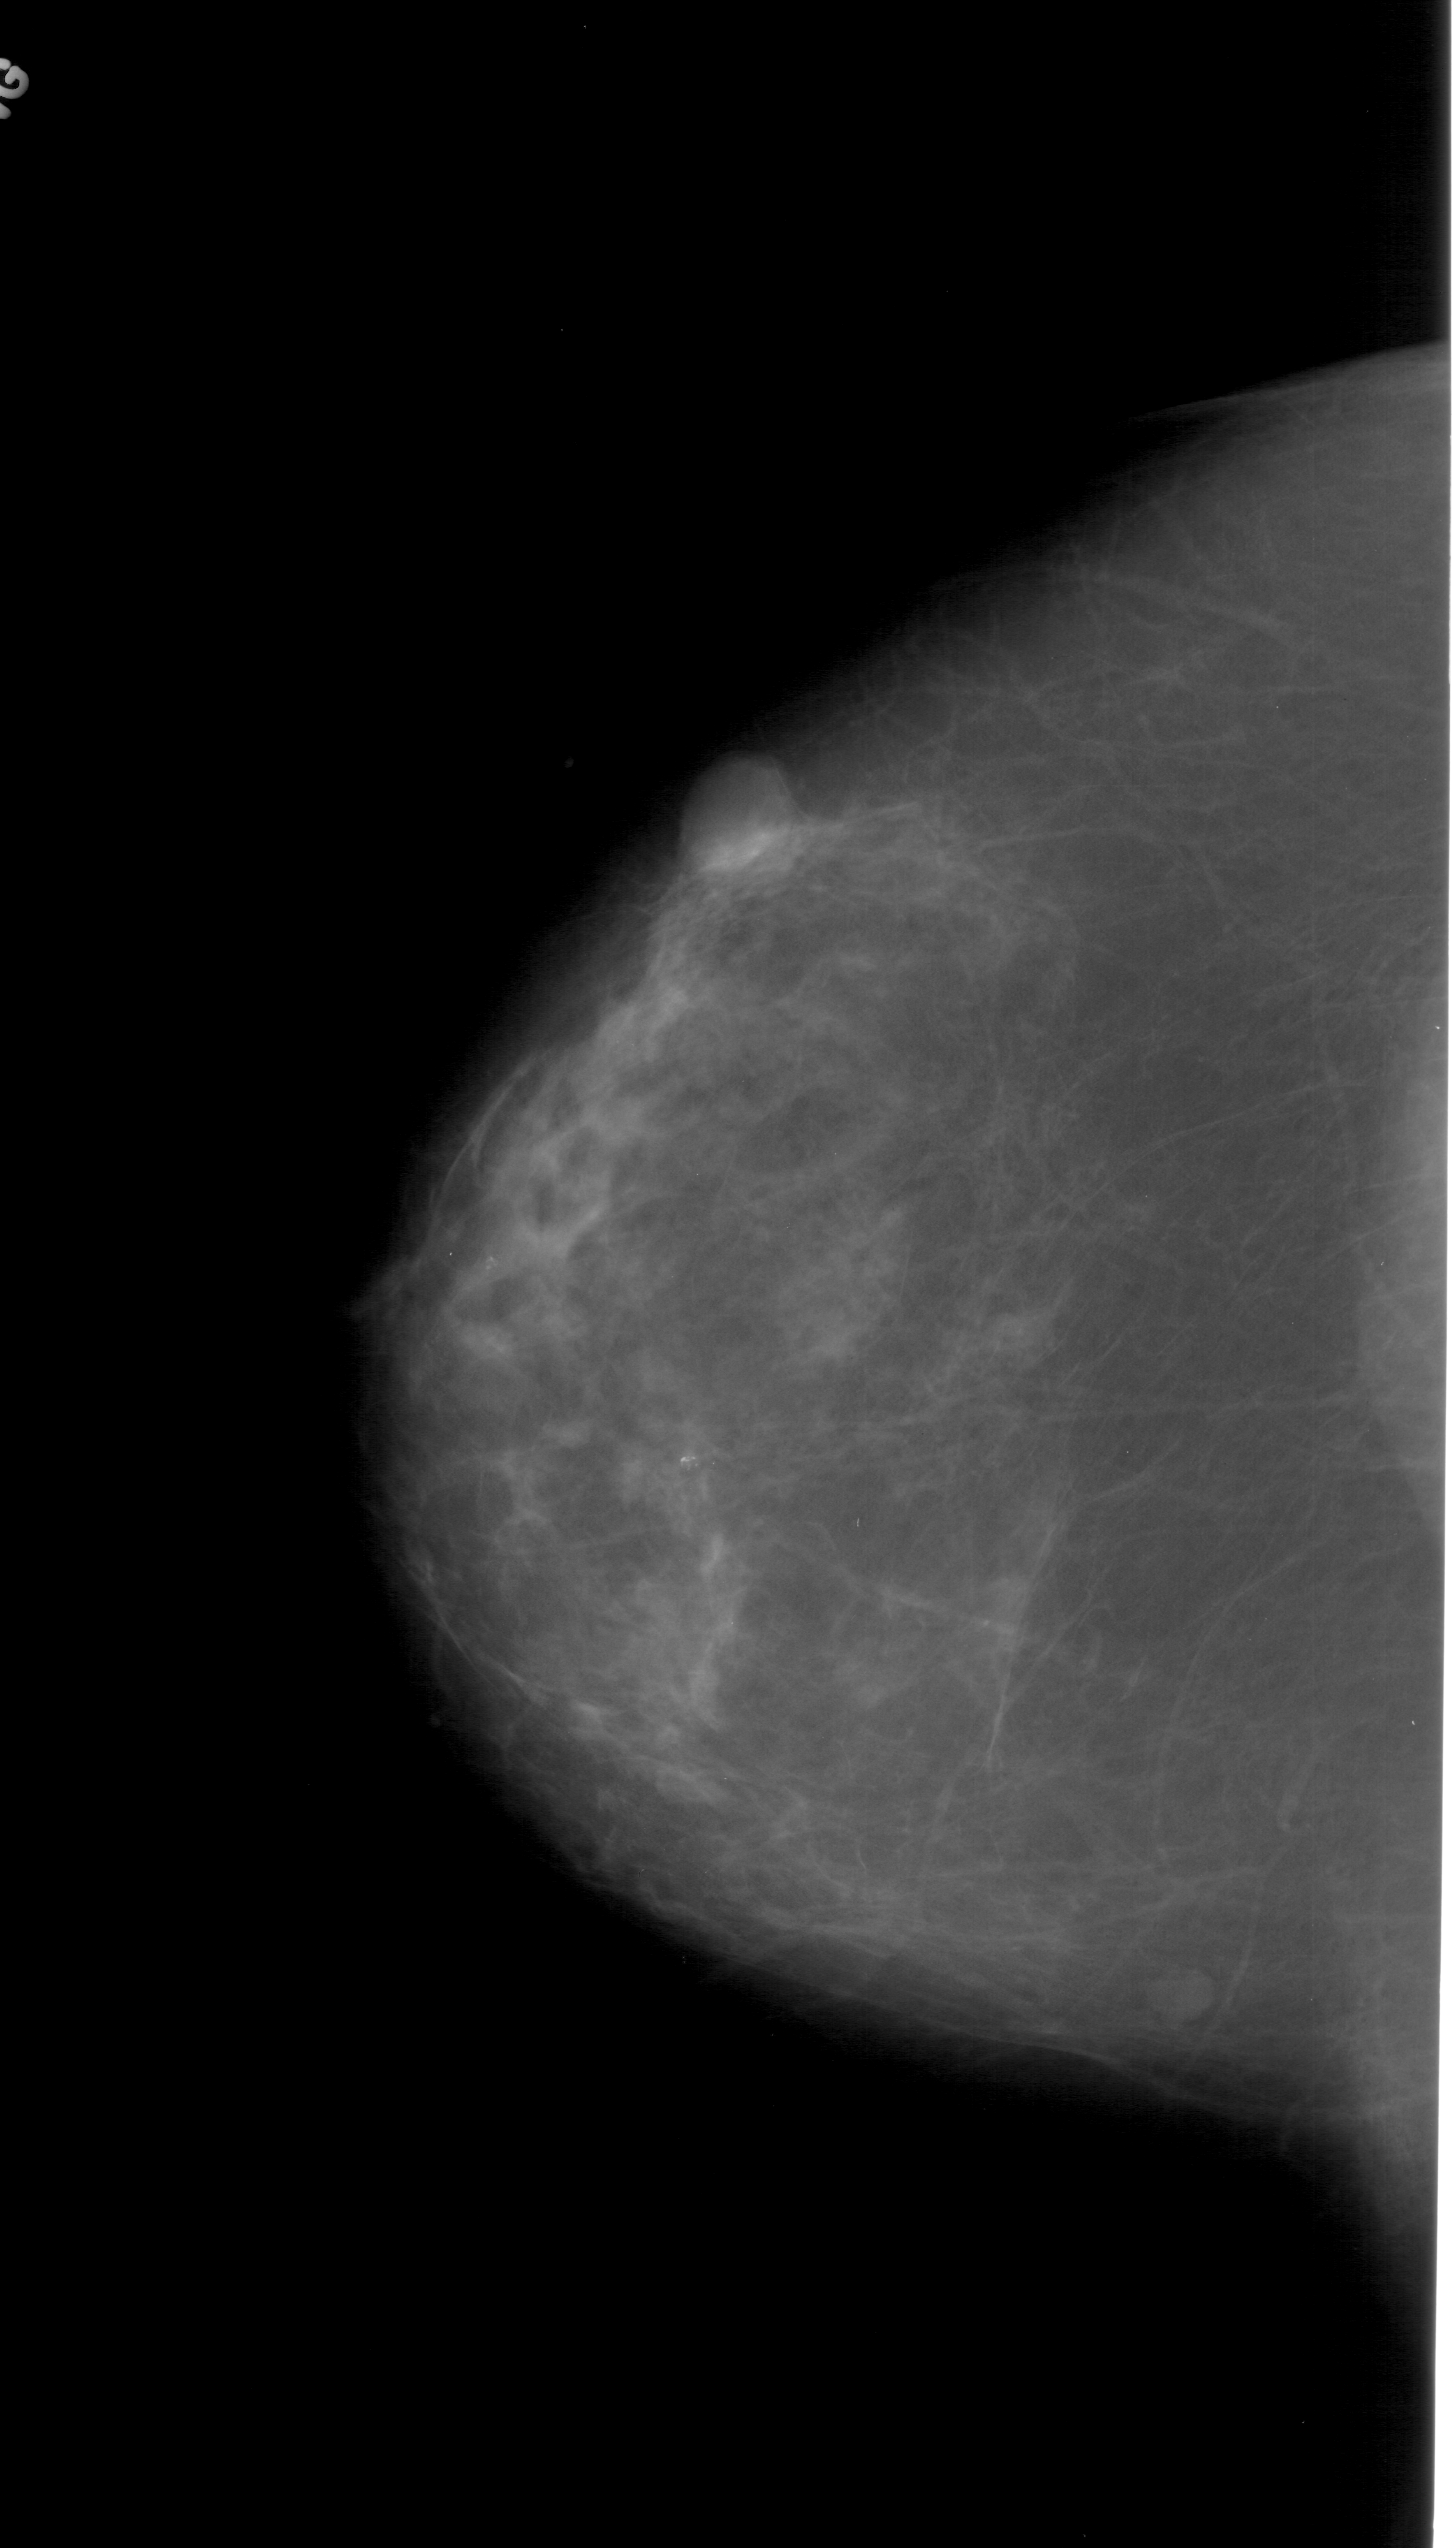
Mammogram (digitized film). Left breast. Craniocaudal (CC) view. BI-RADS breast density category 2 (scale 1–4). 1456 × 2548 image matrix.
Expert-marked regions of interest on this film, with their recorded descriptors:
- mass, shape lobulated, margins circumscribed; BI-RADS assessment category 4; subtlety rating 5 on a 1 (subtle) to 5 (obvious) scale; pathology result (as recorded, not read from the image): benign: bounding box [x1, y1, x2, y2] px = [652, 718, 816, 885]